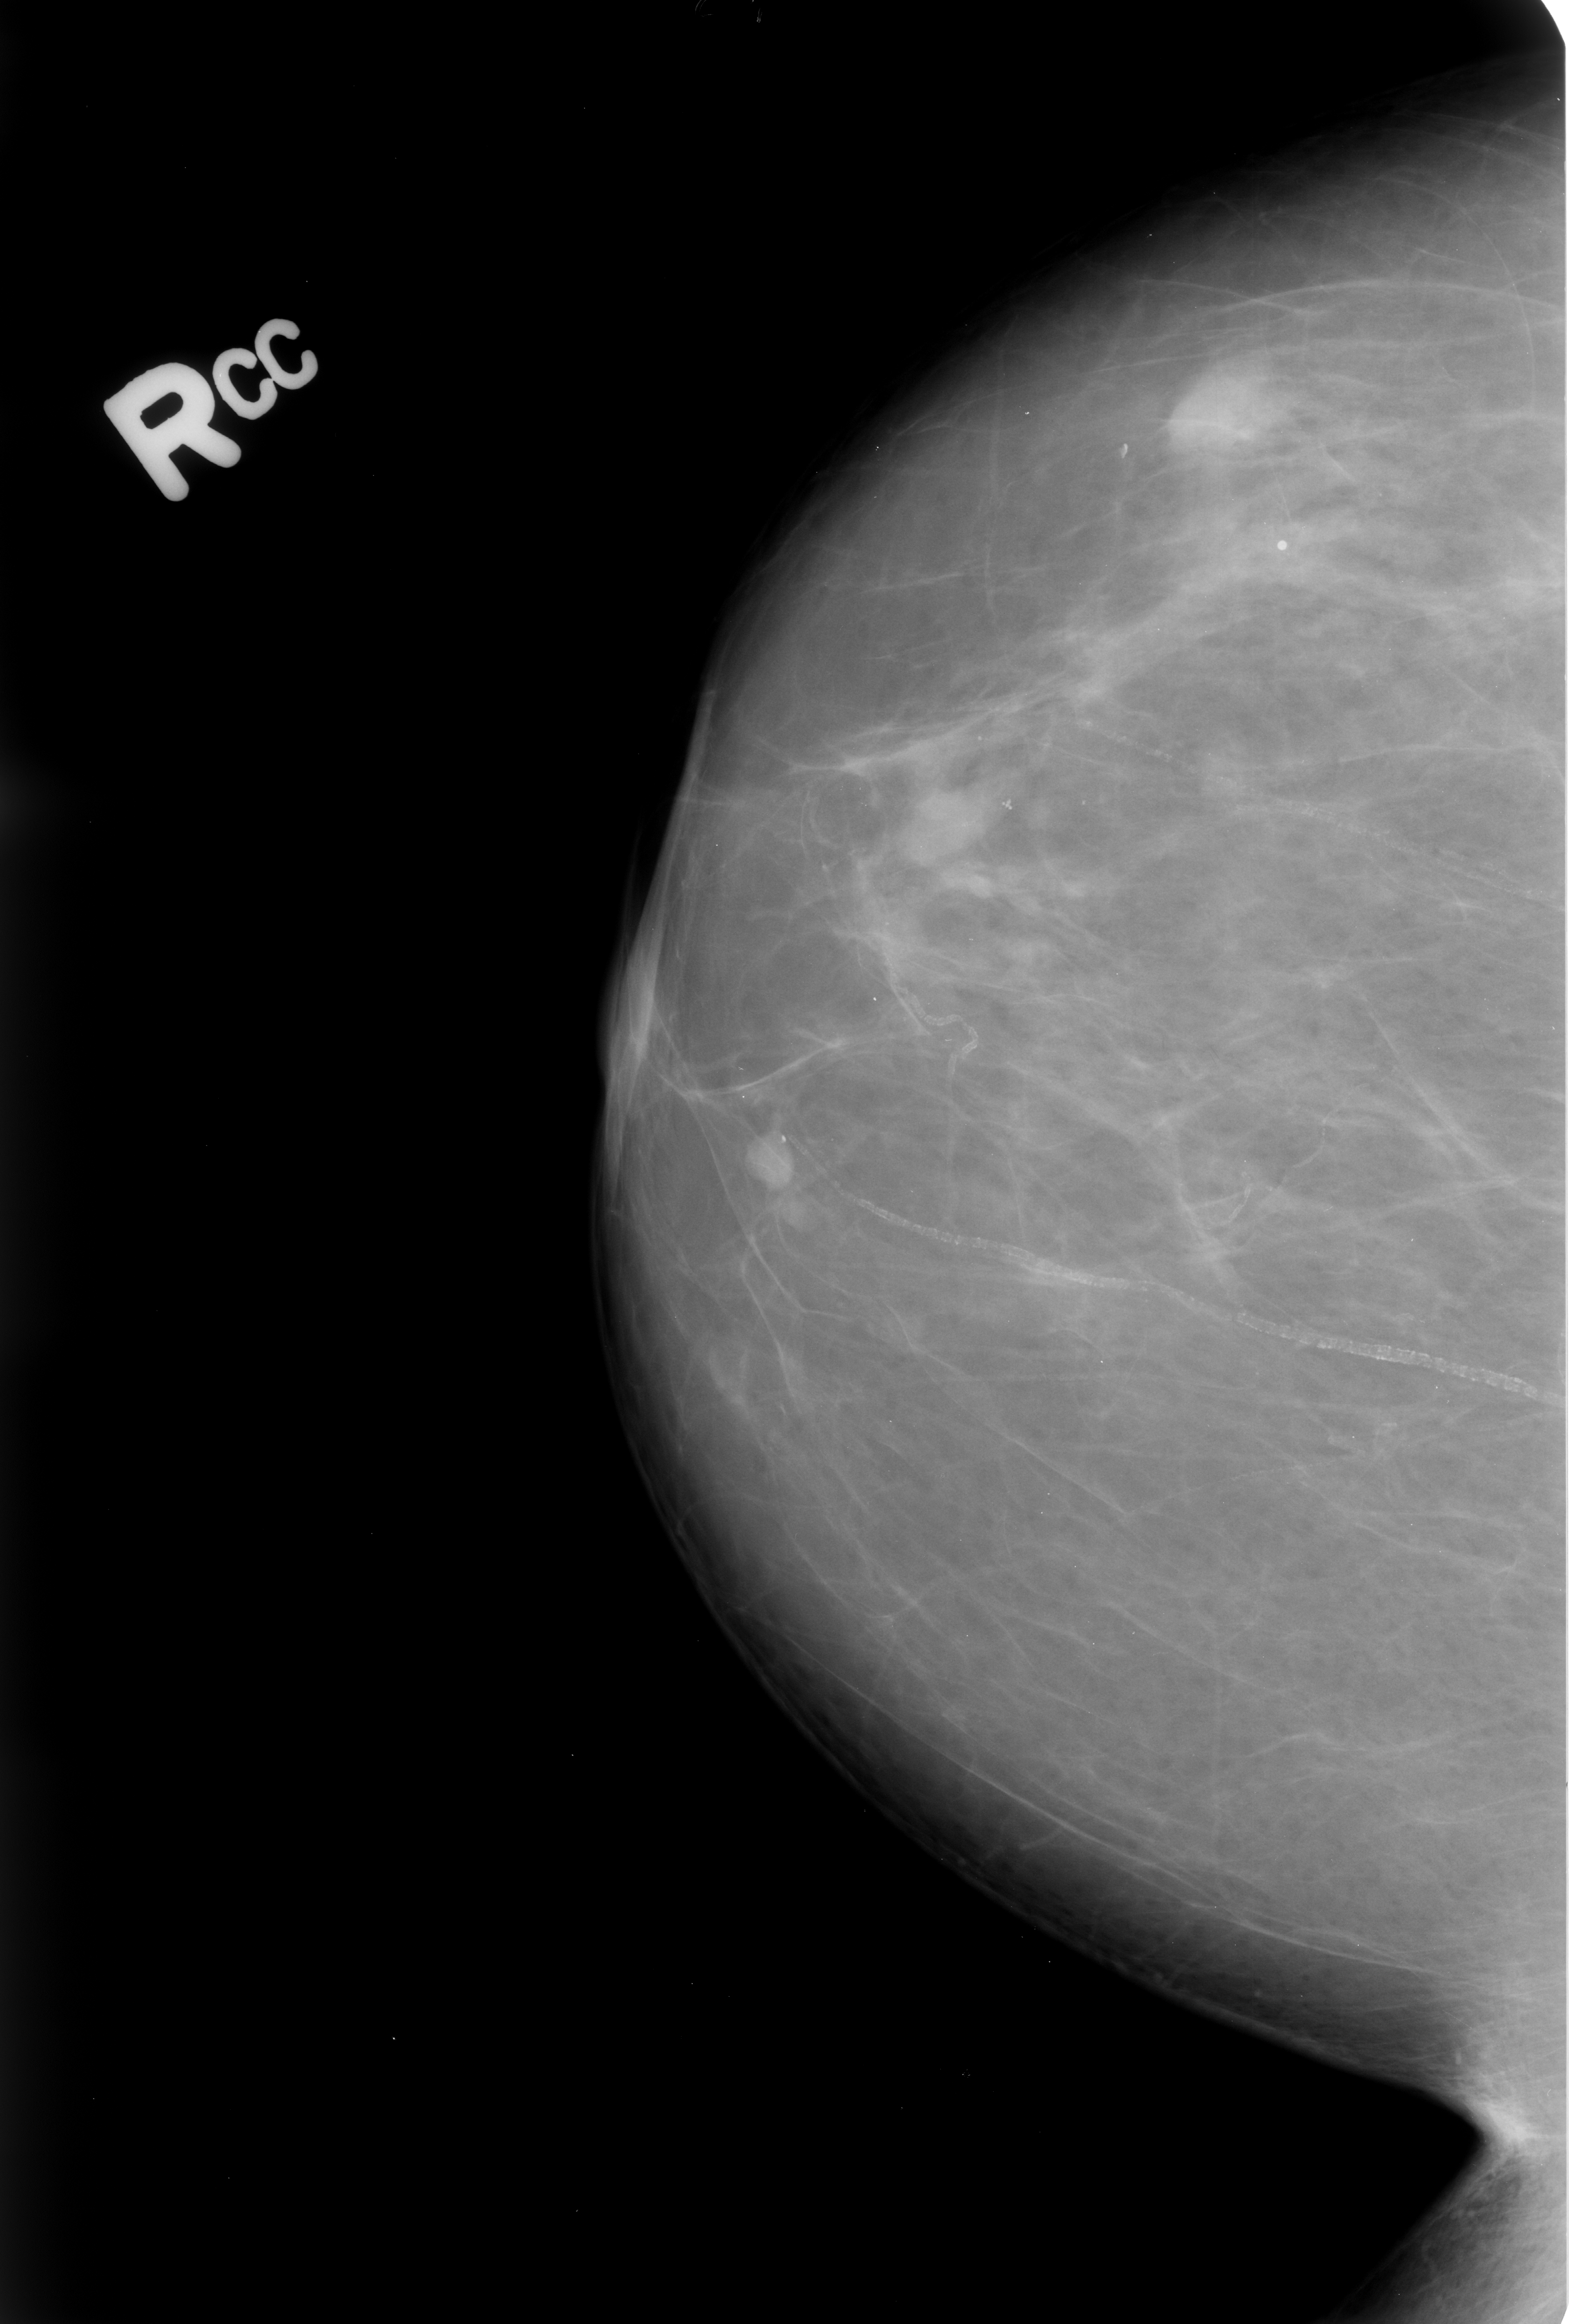
Mammogram (digitized film). Right breast. Craniocaudal (CC) view. BI-RADS breast density category 2 (scale 1–4). 1574 × 2324 image matrix.
Marked abnormalities (boxes around the expert regions of interest):
- mass, shape asymmetric breast tissue; BI-RADS assessment category 2; benign; no additional work-up was recommended (outcome (as recorded, no biopsy): benign without callback): bounding box [x1, y1, x2, y2] px = [1164, 343, 1286, 453]